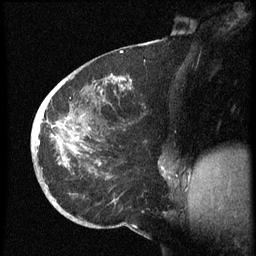
Breast MRI (dynamic contrast-enhanced), one sagittal slice; dynamic contrast-enhanced series, image 2 of 3 at this slice position (ordered by acquisition); 1.5 T; TE 4.2 ms, TR 8.4 ms; 2.5 mm slice thickness; 256 × 256 image matrix, field of view 200 × 200 mm. Patient: female, 38 years. Case-level facts recorded for this patient, not image findings: setting: breast cancer imaged before/during neoadjuvant chemotherapy; receptor status: HER2-positive.
Structures marked on this image (semi-automatically segmented with operator editing):
- analysis volume of interest (the breast-tissue region the enhancement analysis was run in; not a lesion): box from (x=32, y=74) to (x=173, y=202) px
- tumour enhancement mask (voxels above the 70 % enhancement threshold inside the analysis volume of interest): (x=36, y=76)–(x=166, y=172)